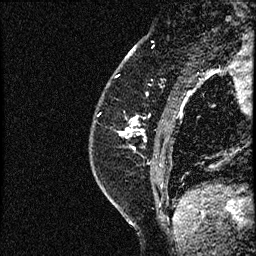
Breast MRI (dynamic contrast-enhanced), one sagittal slice. Position 16 of 52 along the scan axis. Dynamic contrast-enhanced study with each time point stored as its own series, time point 2 of 3 at this slice position (early post-contrast, ordered by acquisition time). 1.5 T. TE 4.2 ms, TR 17.6 ms. 2 mm slice thickness. 256 × 256 image matrix. Female patient, age 49 years. From the clinical record (not read from this slice): setting: breast cancer imaged before/during neoadjuvant chemotherapy; receptor status: HER2-positive.
Outlined on this slice (semi-automatically segmented with operator editing):
- analysis volume of interest (the breast-tissue region the enhancement analysis was run in; not a lesion): bounding box [x1, y1, x2, y2] px = [90, 65, 182, 175]
- tumour enhancement mask (voxels above the 100 % enhancement threshold inside the analysis volume of interest): [122, 118, 137, 137]